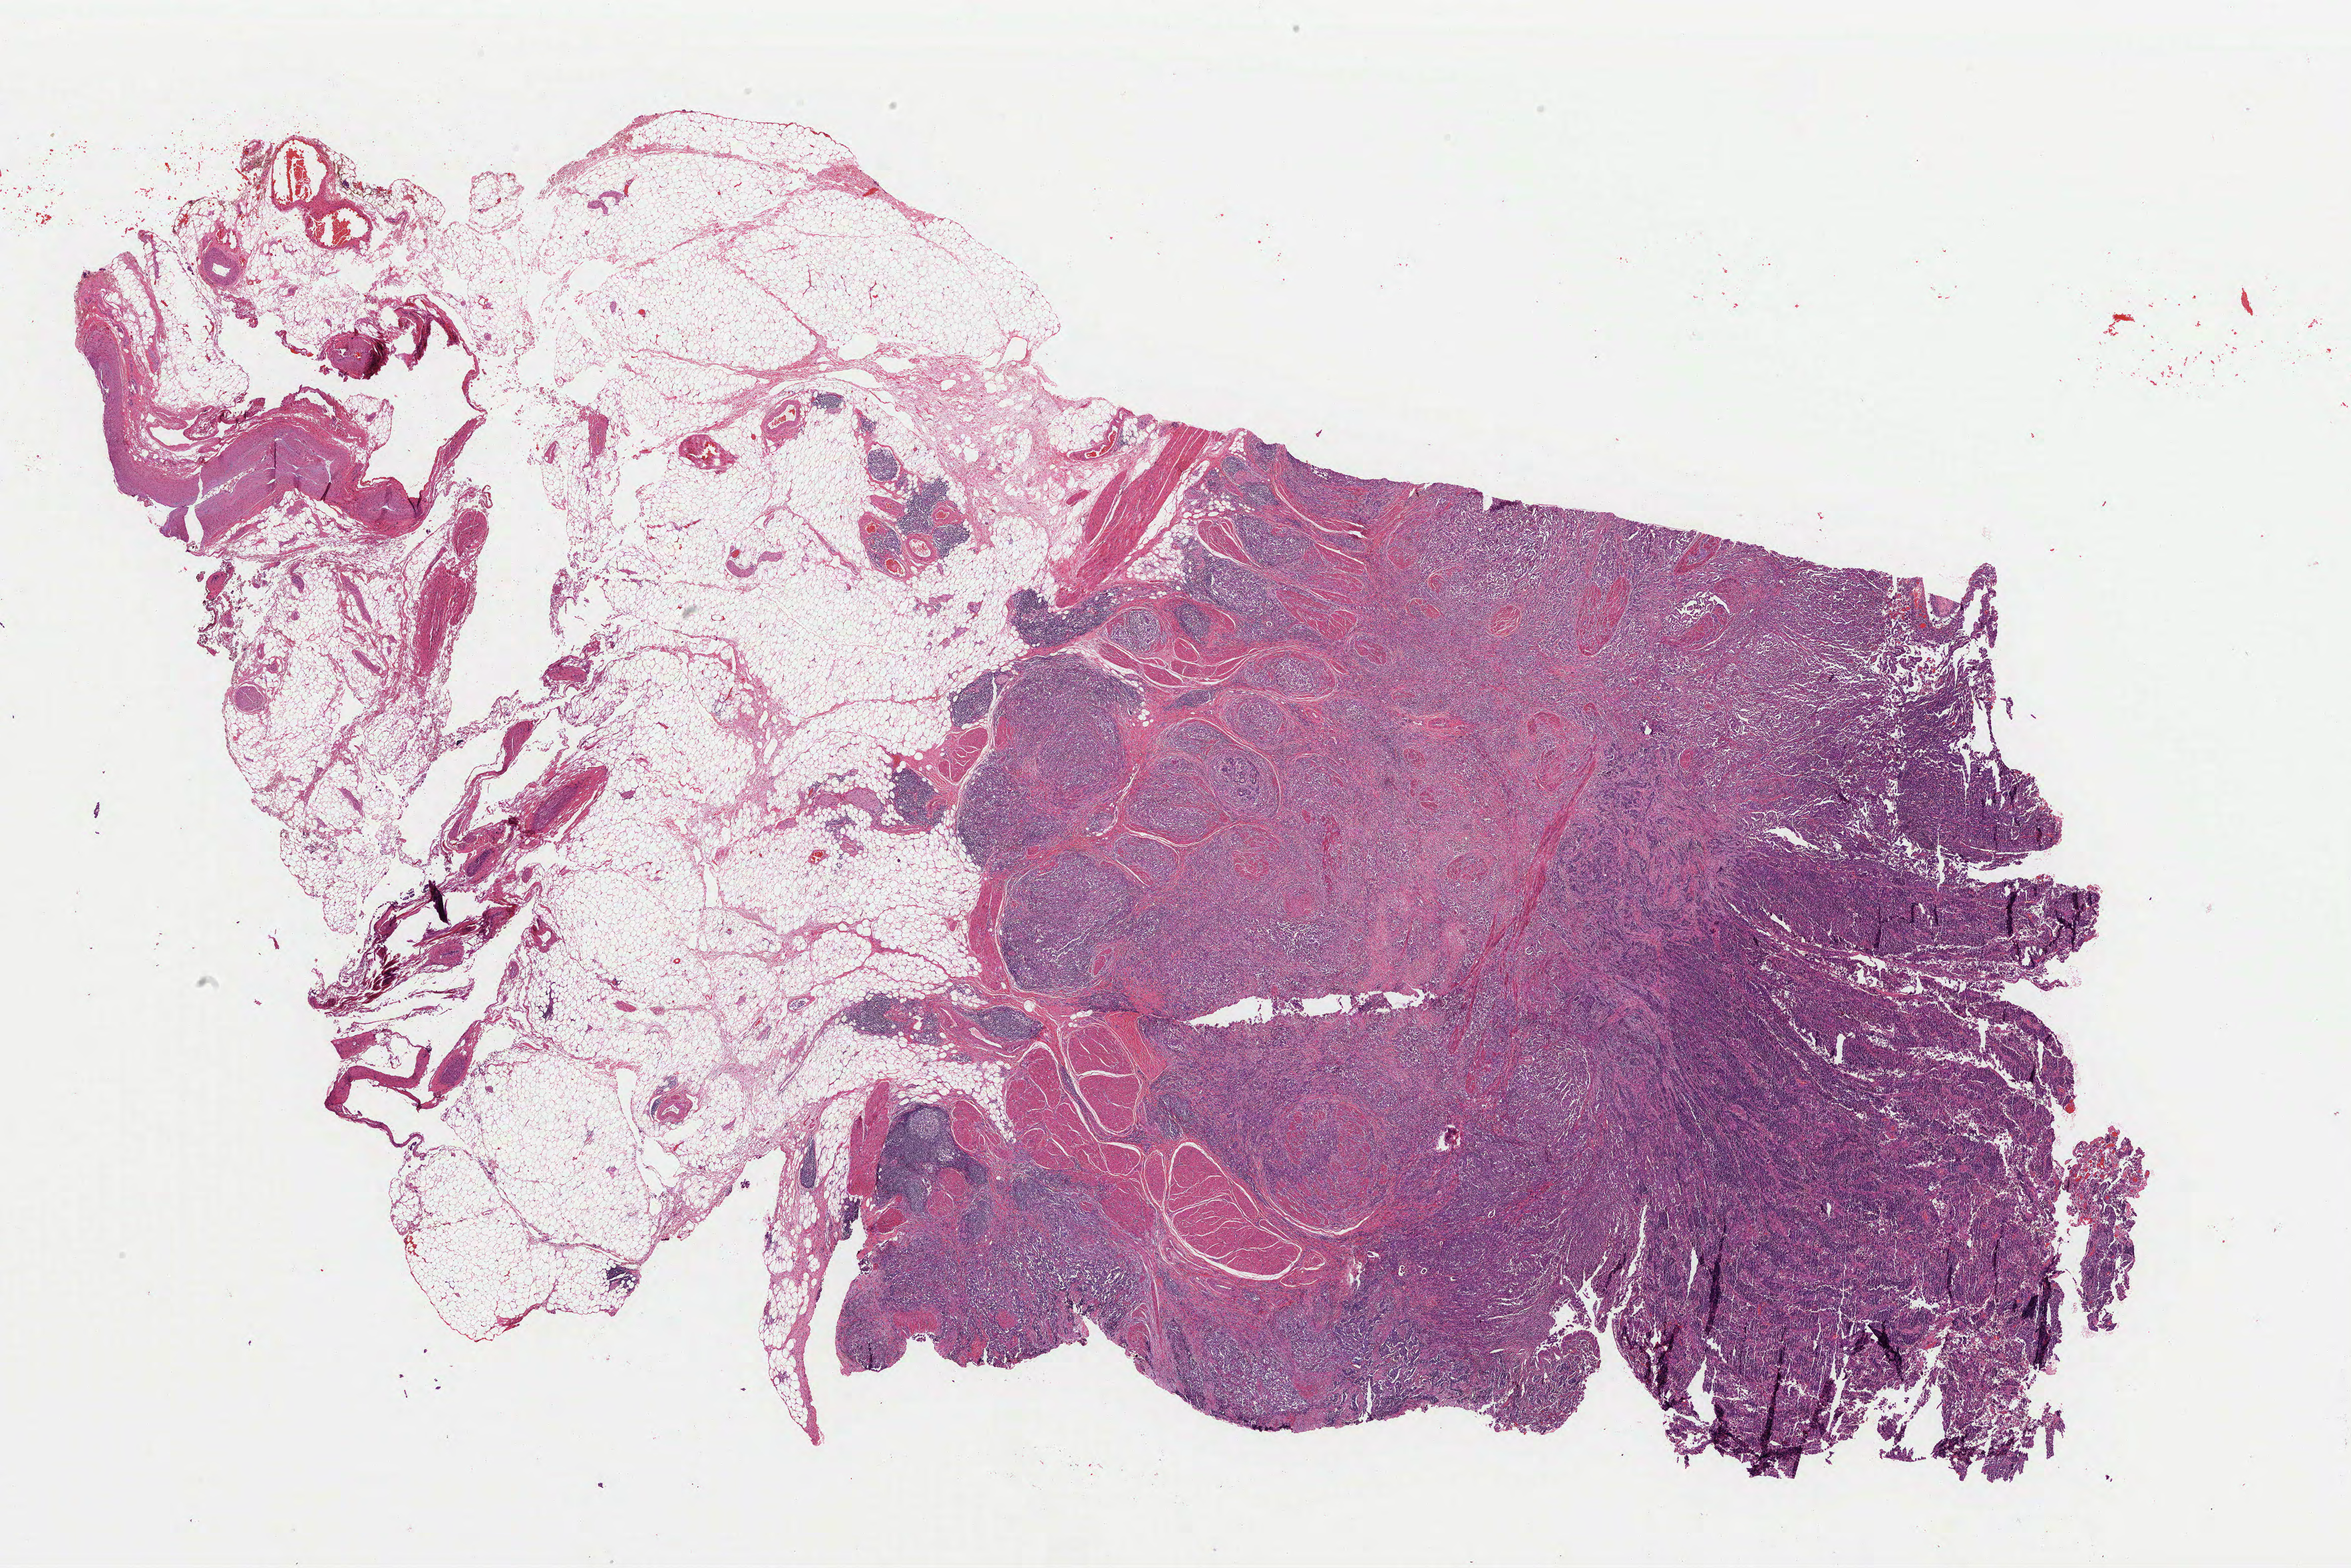
Whole-slide histology image, Hematoxylin and eosin (H&E) stained, whole scanned area (about 28.0 x 18.7 mm) shown as a low-resolution overview, formalin-fixed paraffin-embedded (FFPE) diagnostic section, primary tumour sample from the bladder. Male, age 59 years at initial diagnosis. Histologic grade: high grade.
AJCC pathologic stage: III (7th edition). Histologic diagnosis: Transitional cell carcinoma.